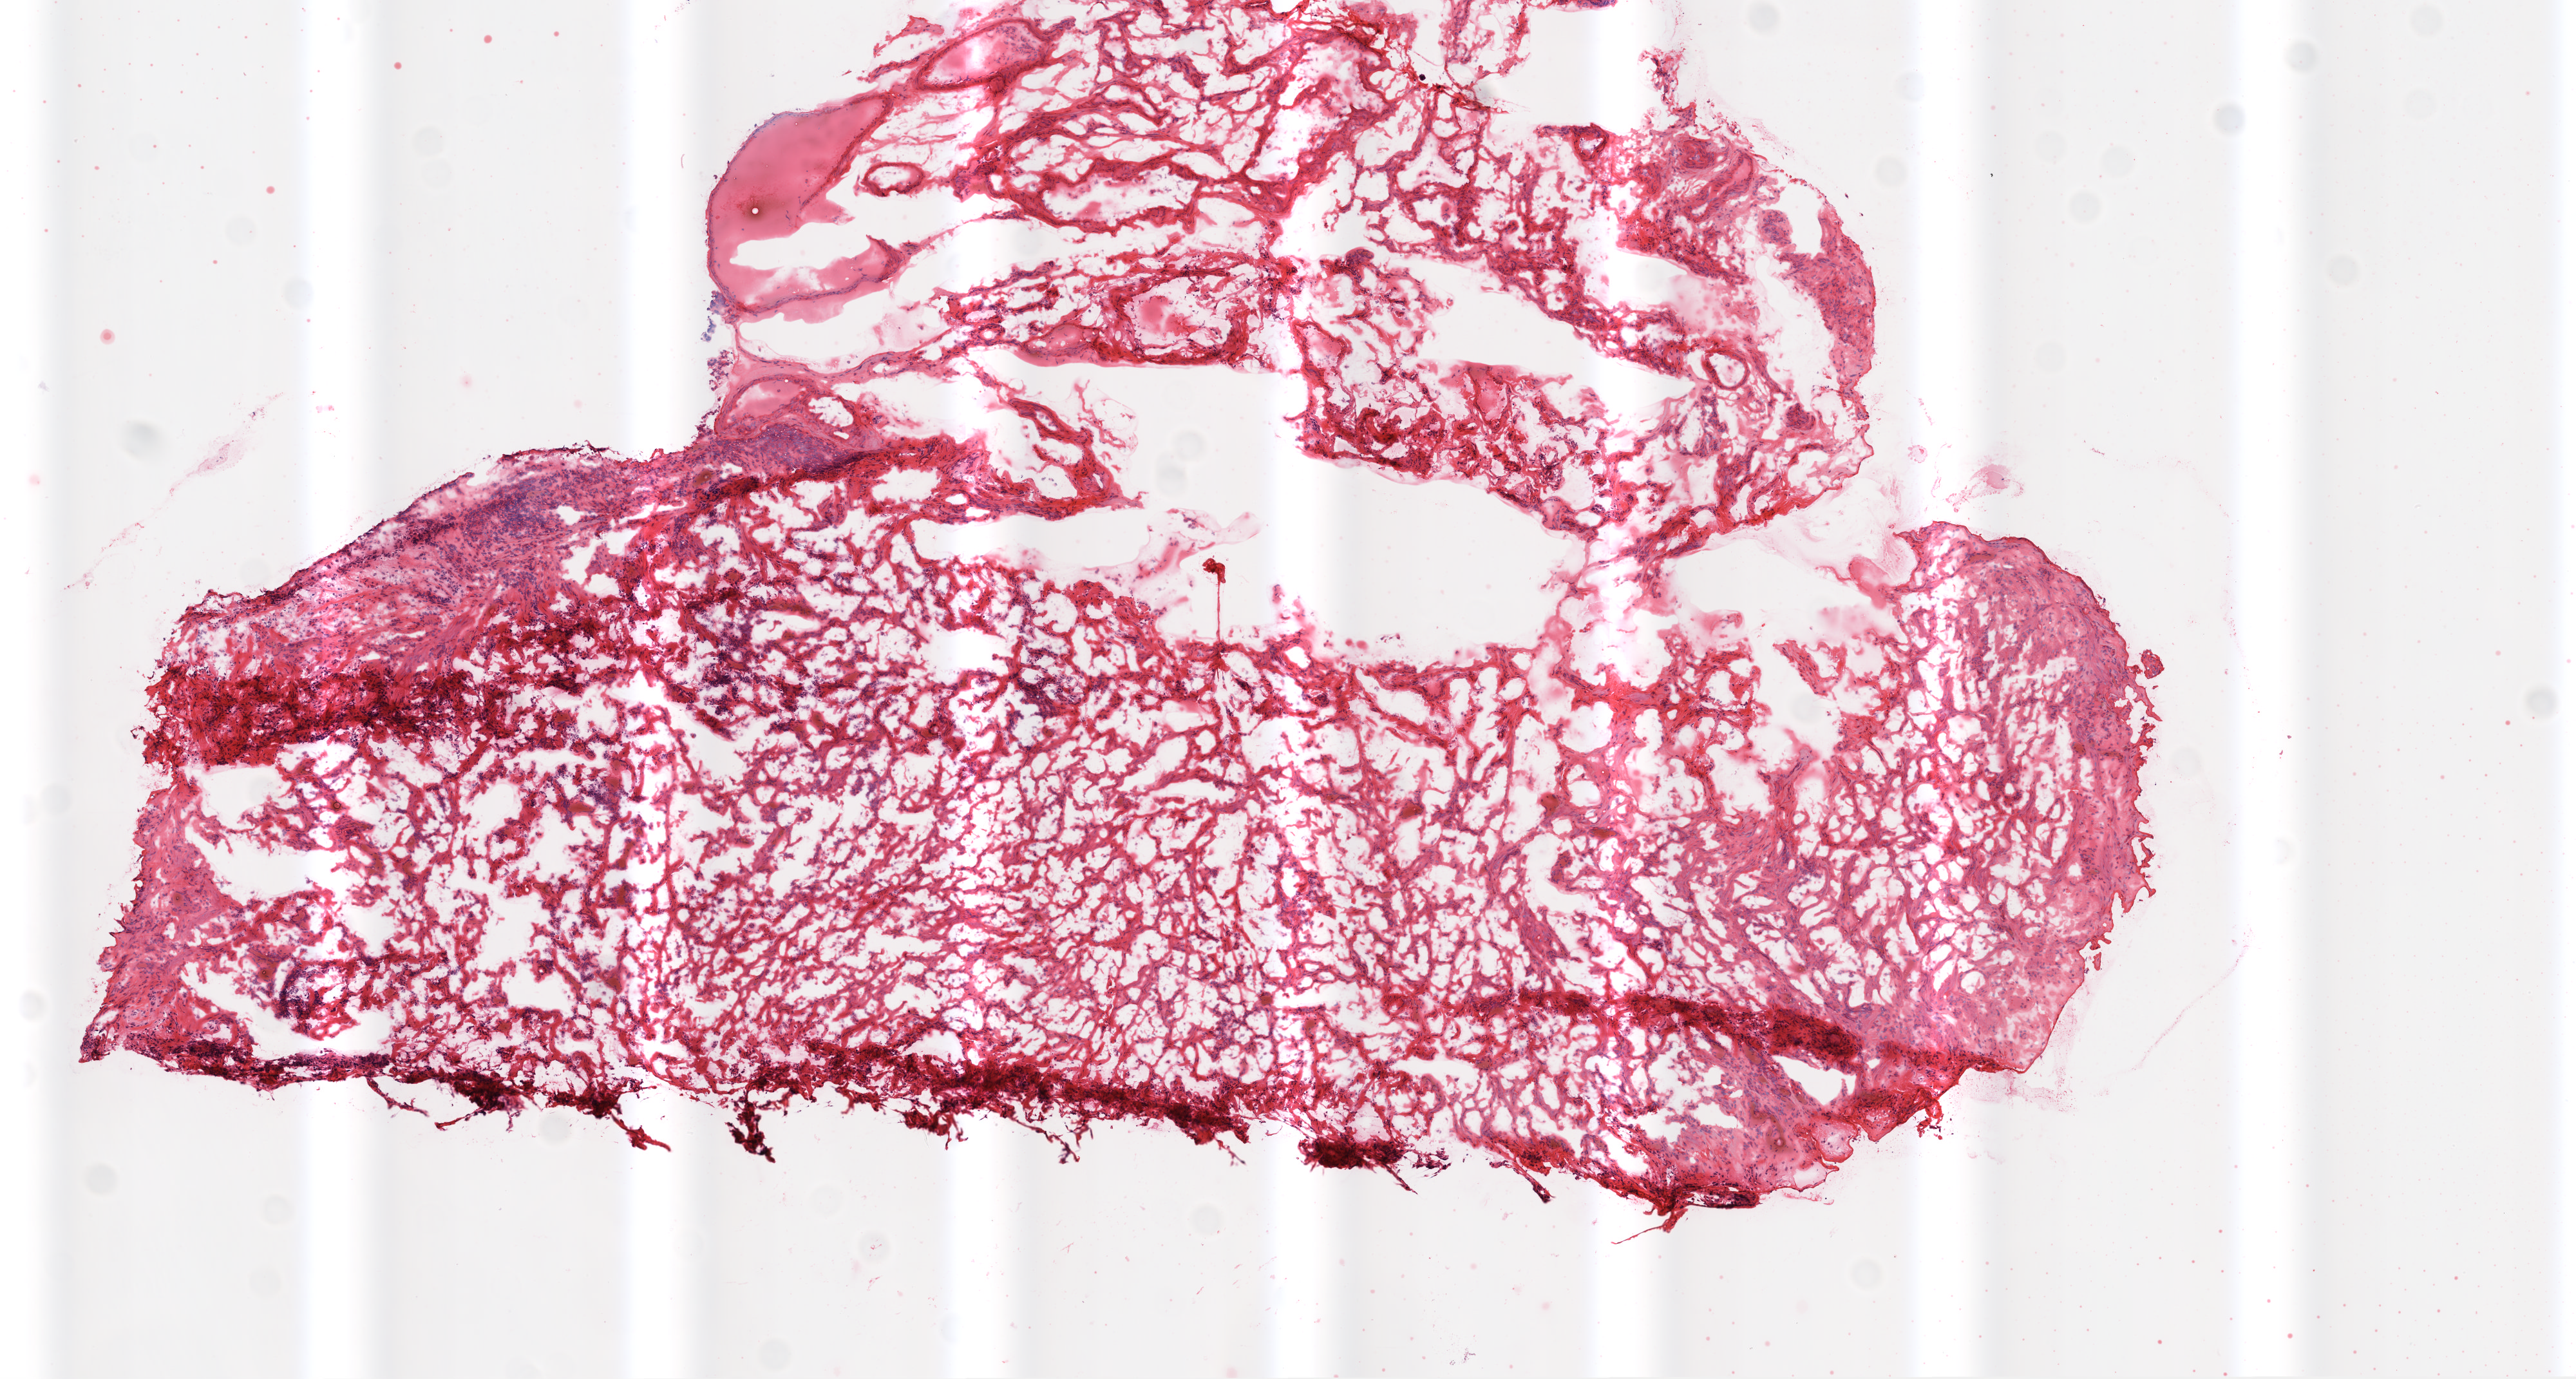
Digitized H&E-stained tissue section (whole slide), low-resolution overview of the scanned area, about 8.0 x 4.3 mm. Frozen section. Ovary, solid tissue normal (non-tumour tissue) sample. Patient: female, age at initial diagnosis 40 years.
This section: solid tissue normal (non-tumour) sample from the same patient. Patient diagnosis: Serous cystadenocarcinoma, NOS.